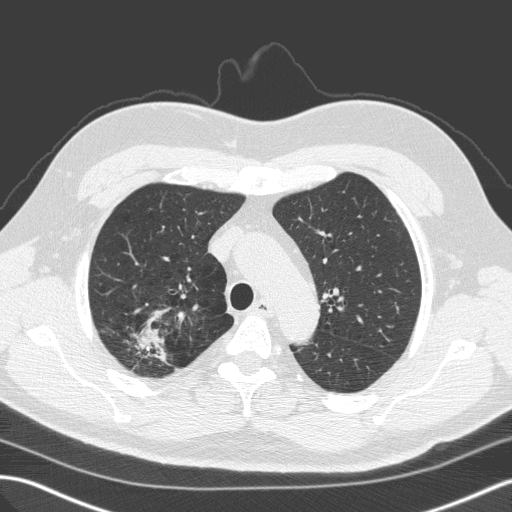
Axial slice from a low-dose chest CT screening exam. First (baseline) screen. Lung window (W 1500 / L -600 HU). 2 mm slice thickness. Male, age 59 years at enrolment.
- Expert reader's lesion annotation, box from (x=117, y=309) to (x=178, y=373) px.
- The exam's reader record, not a measurement of the box and not confirmed to be the same lesion: non-calcified nodule or mass ≥4 mm, right upper lobe, 28 × 25 mm, spiculated (stellate) margins, soft tissue attenuation.
- Official screen result: positive, change unspecified: nodule(s) >= 4 mm or enlarging nodule(s), mass(es), or other non-specific abnormalities suspicious for lung cancer.
- Participant outcome: lung cancer diagnosed 64 days after this screen — large cell carcinoma, NOS, right upper lobe, undifferentiated (G4), stage IA (AJCC 6th edition), 25 mm at pathology.